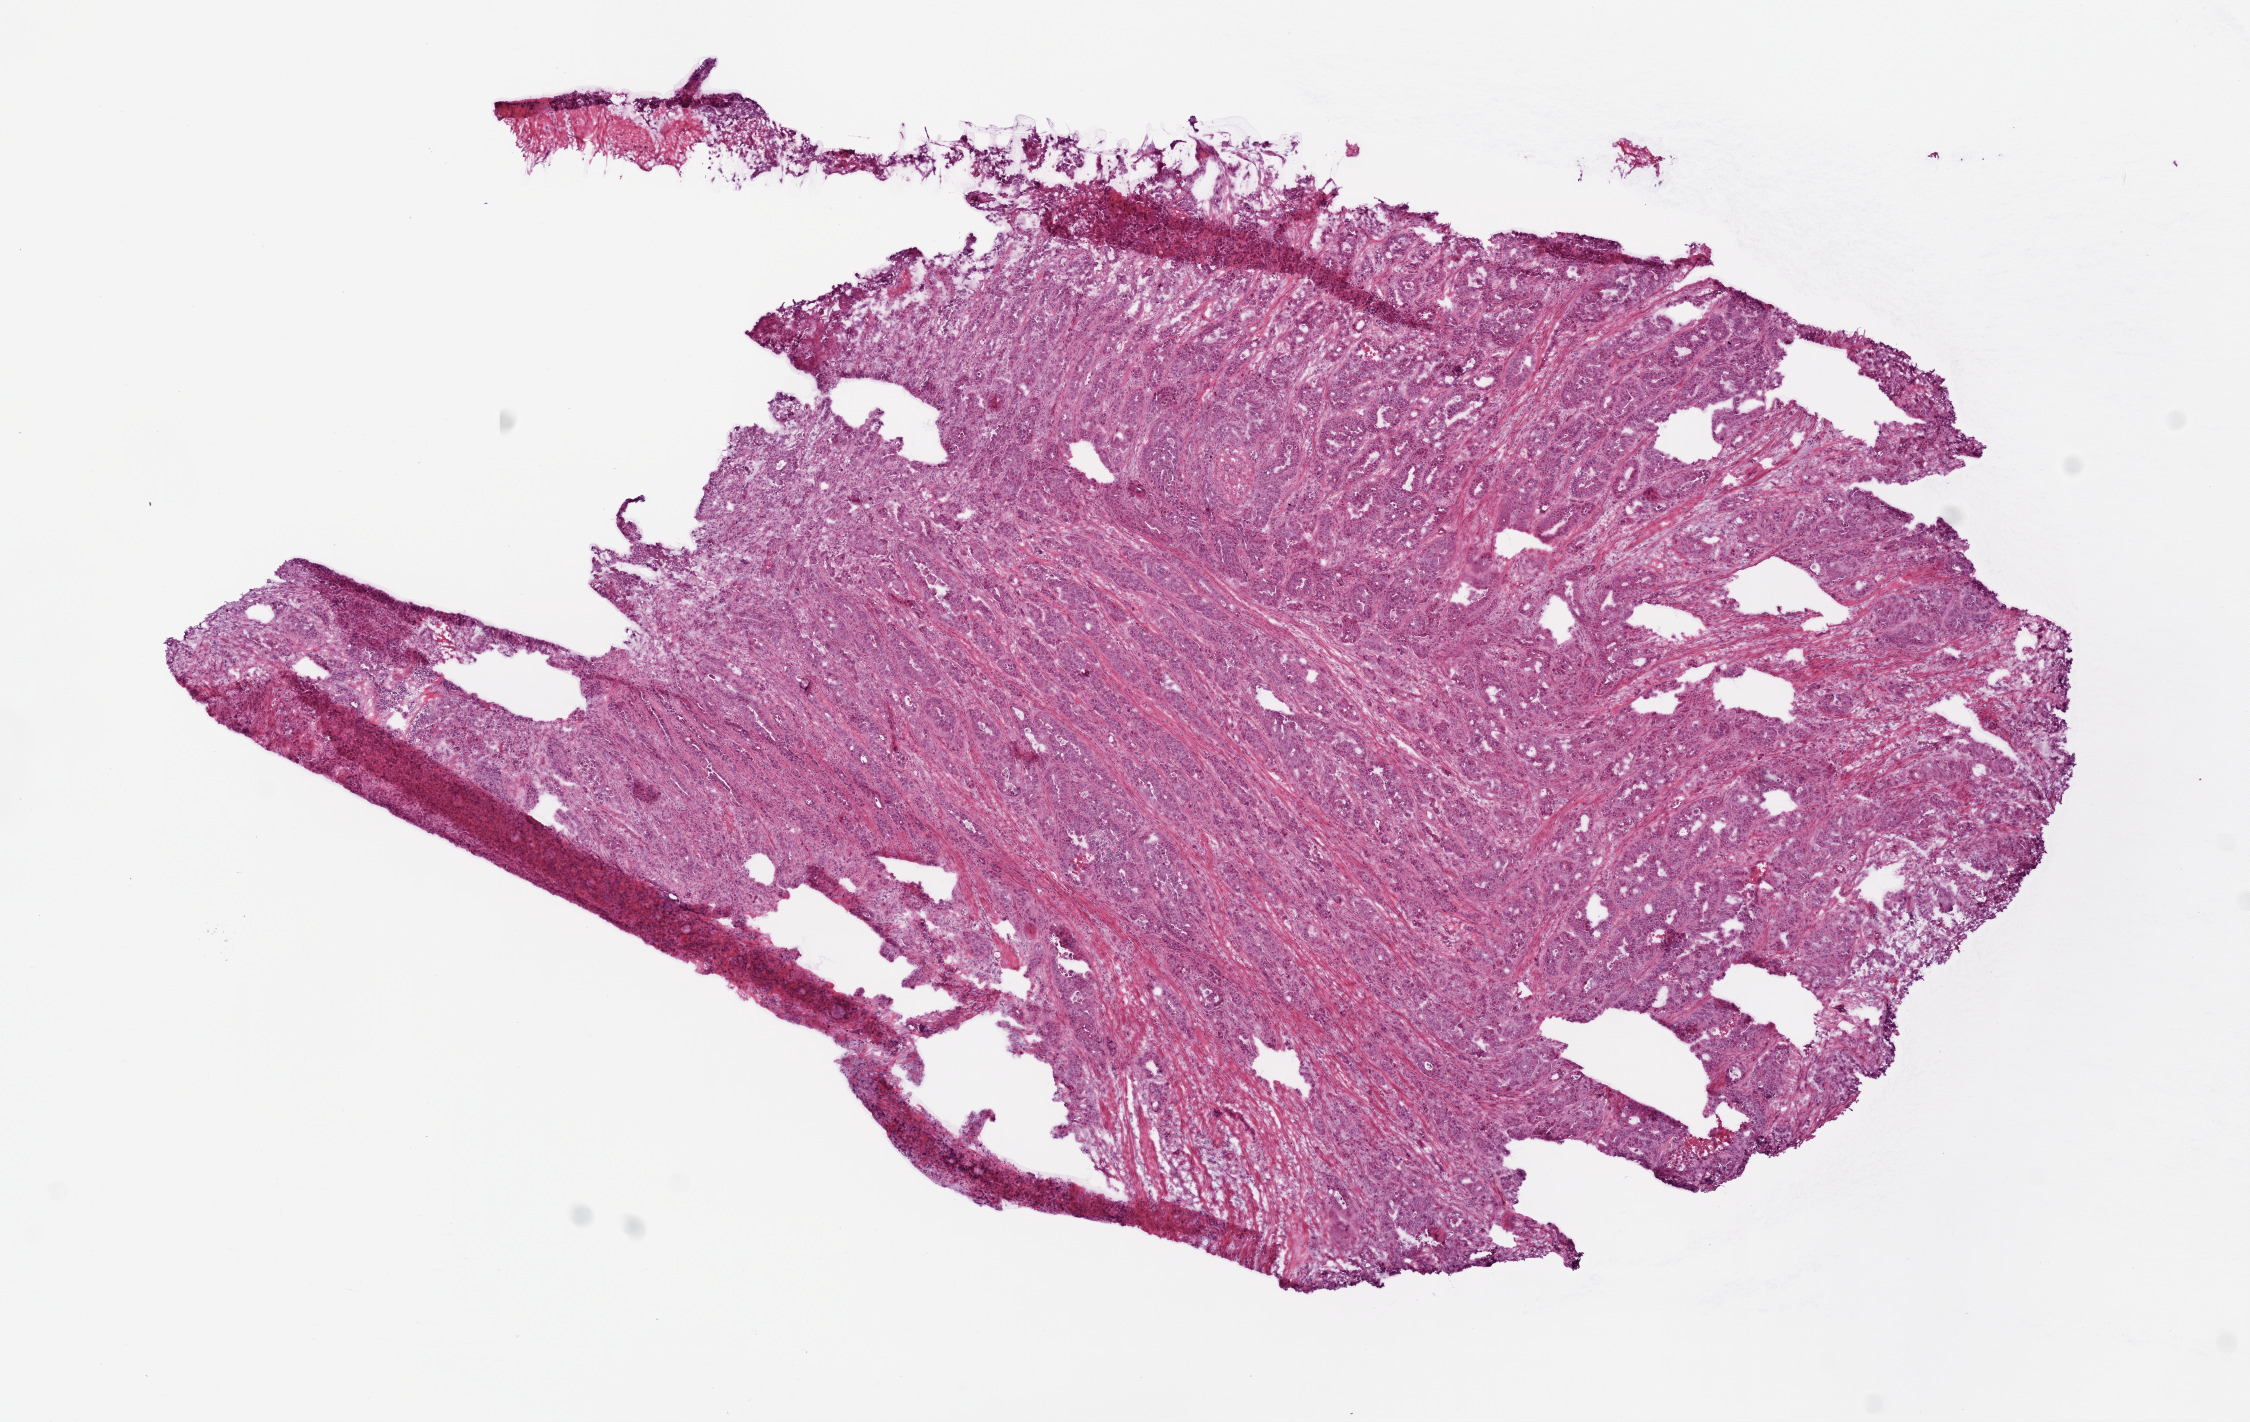
Hematoxylin and eosin (H&E) stained whole-slide image — shown as a low-resolution overview of the whole scanned area (about 9.0 x 5.7 mm, acquisition: 20x scan), frozen section from the top of the tissue portion, primary tumour sample from the colon. Male, age 45 years at initial diagnosis. Composition of this section per pathologist review: tumour cells 85%, tumour nuclei 85%, normal cells 0%, stromal cells 10%, necrosis 5%.
Histologic diagnosis: Adenocarcinoma, NOS. TNM: T4 N2 M1. Lymph nodes positive (case pathology): 23 of 29 examined. AJCC pathologic stage: IV (6th edition).